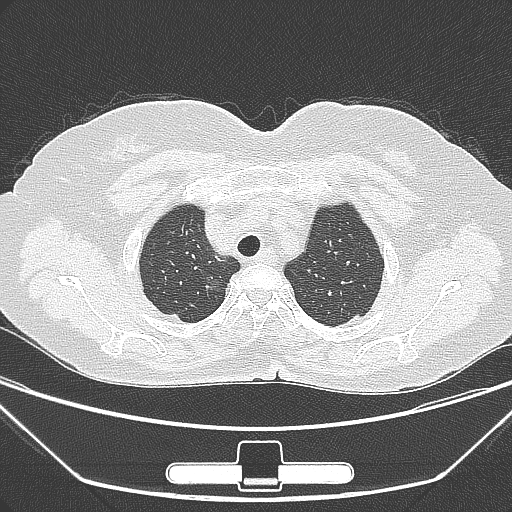
Chest CT, one axial slice; position 235 of 275 along the scan axis; lung window (W 1500 / L -600 HU); 1 mm slice thickness; 512 × 512 image matrix, field of view 356 × 356 mm. Patient: female, 63 years. Case-level facts recorded for this patient, not image findings: clinical TNM (as recorded): T1a N0 M0.
Structures marked on this image (rectangle marked by the reading radiologist):
- lung tumour (recorded histology: adenocarcinoma): bounding box <196,268,235,310> (left, top, right, bottom; pixels)